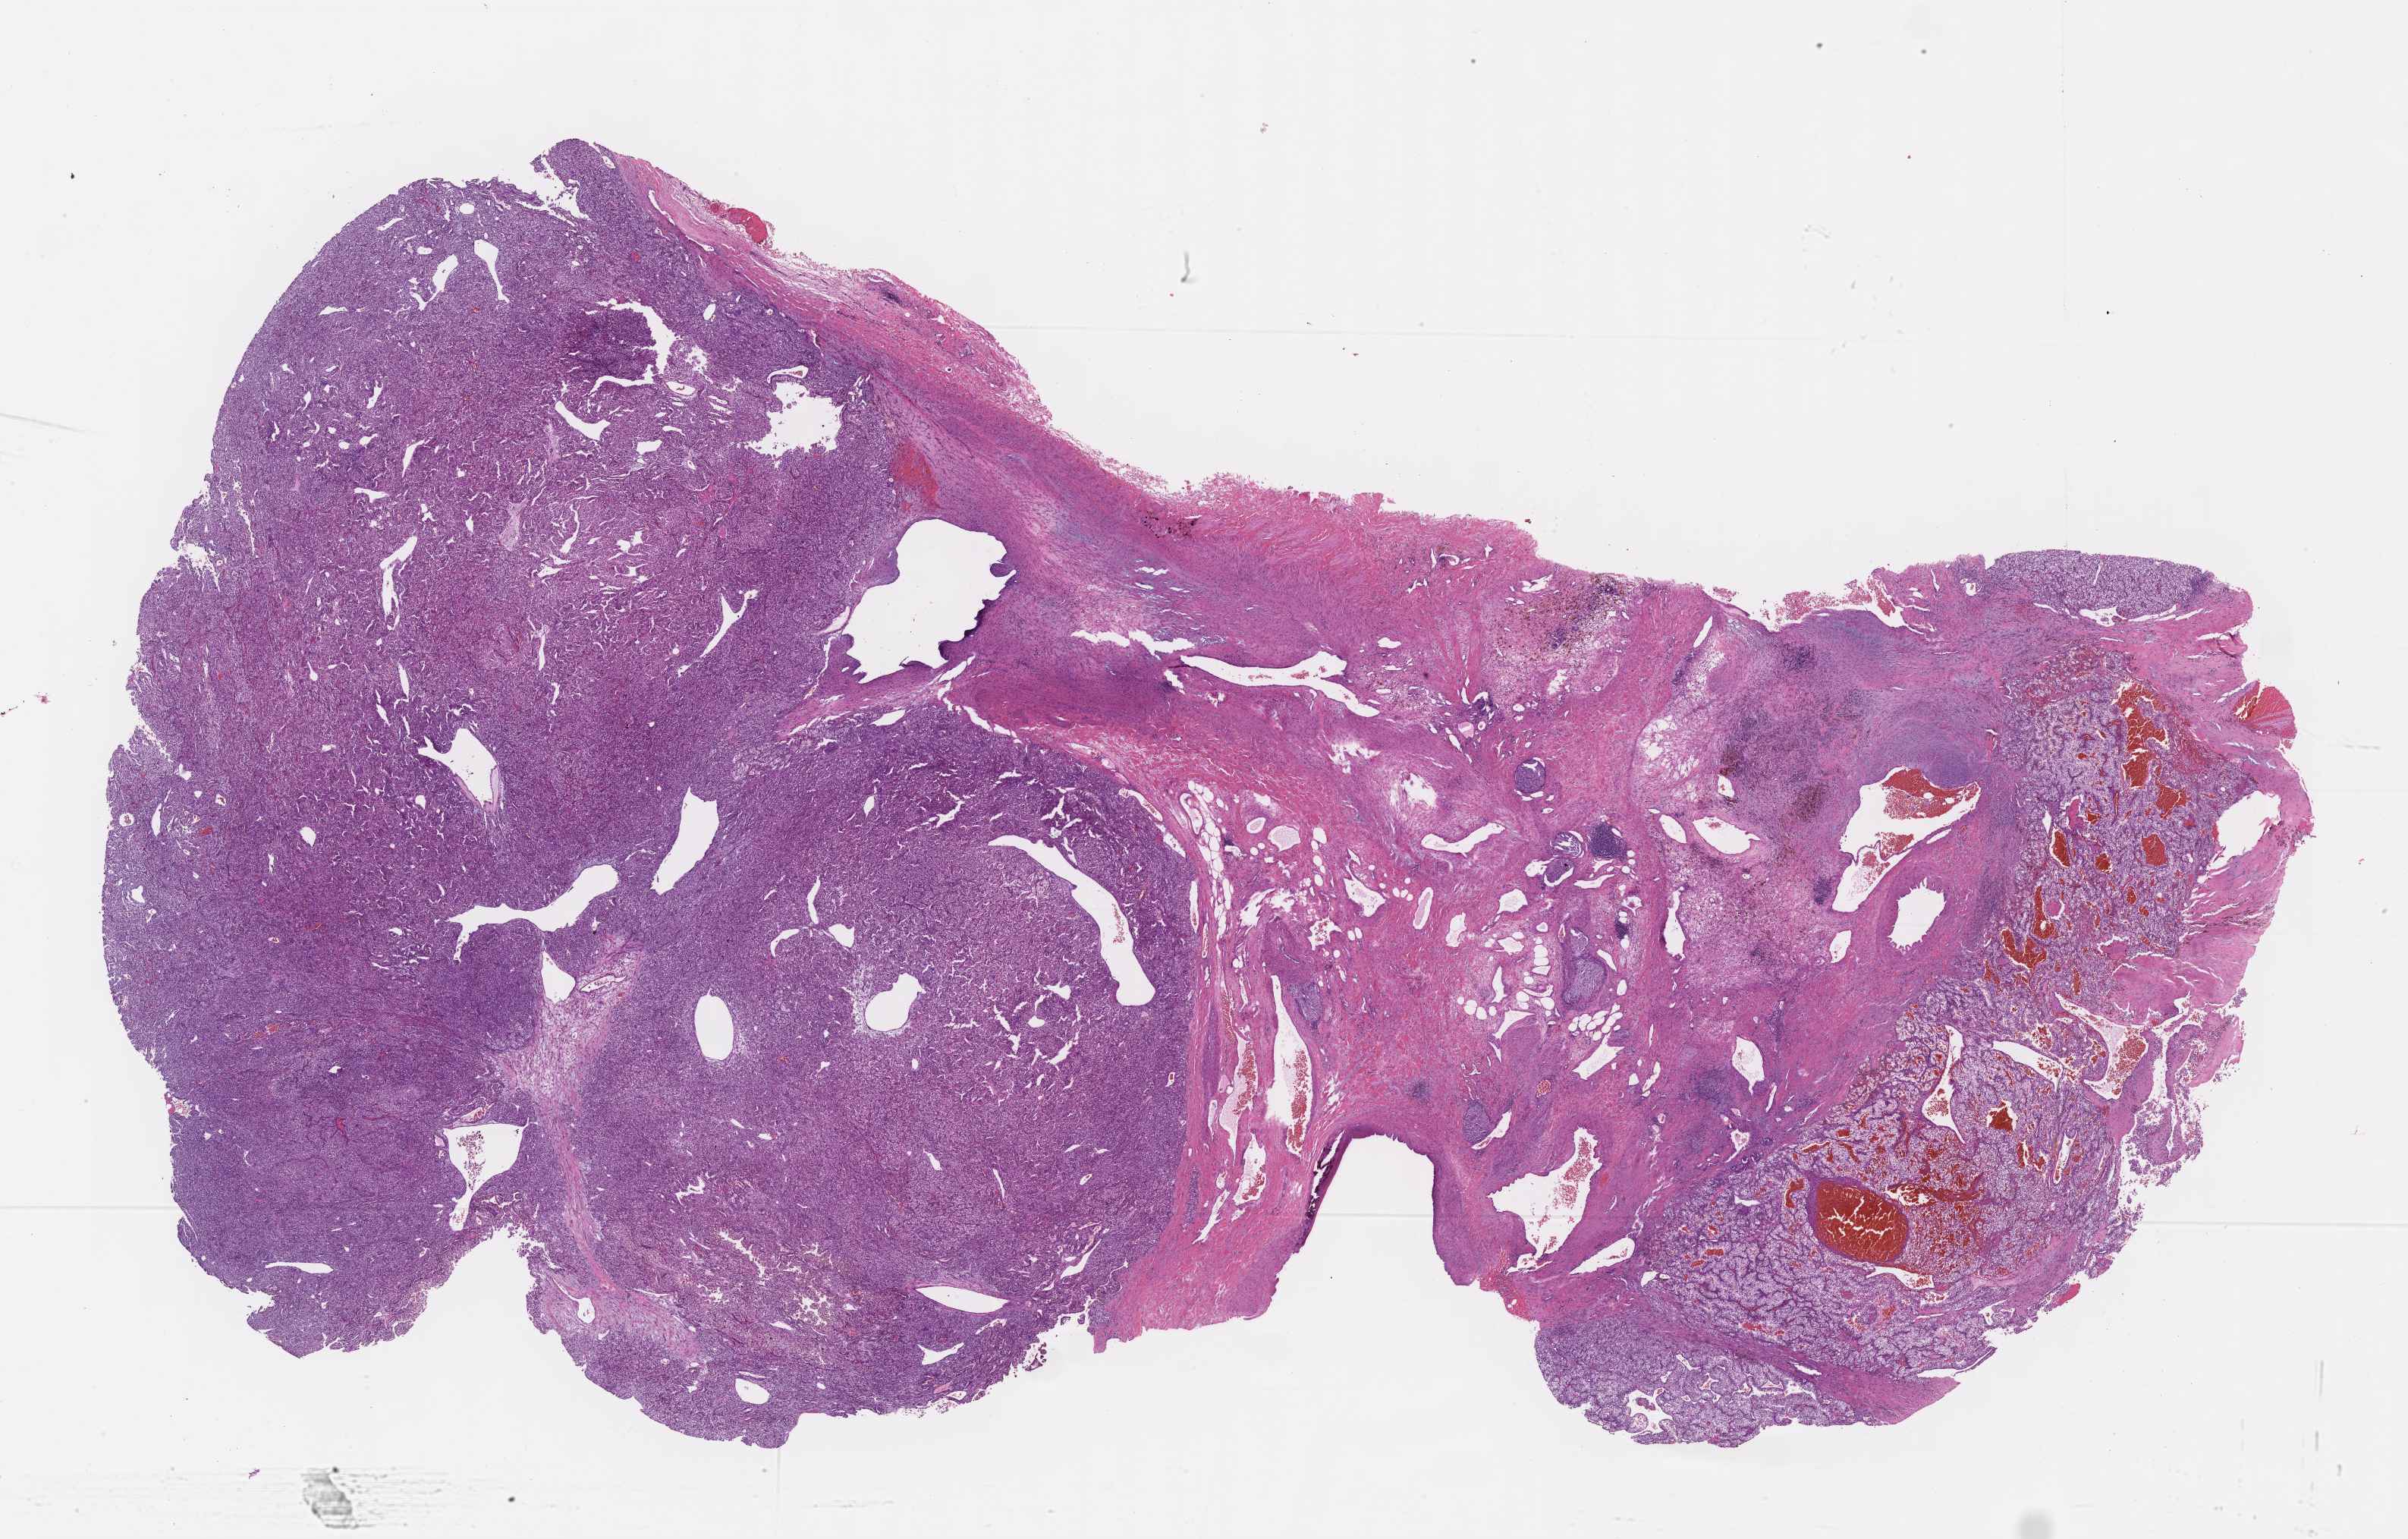
Whole-slide histology image, H&E, a low-resolution overview of the entire scanned area, about 25.7 x 16.4 mm (slide scanned at 40x). Formalin-fixed paraffin-embedded (FFPE) diagnostic section. Kidney, primary tumour sample. Male, age 67 years at initial diagnosis. Histologic grade: G3 (poorly differentiated).
AJCC pathologic stage: IV (7th edition). Histologic diagnosis: Clear cell adenocarcinoma, NOS.